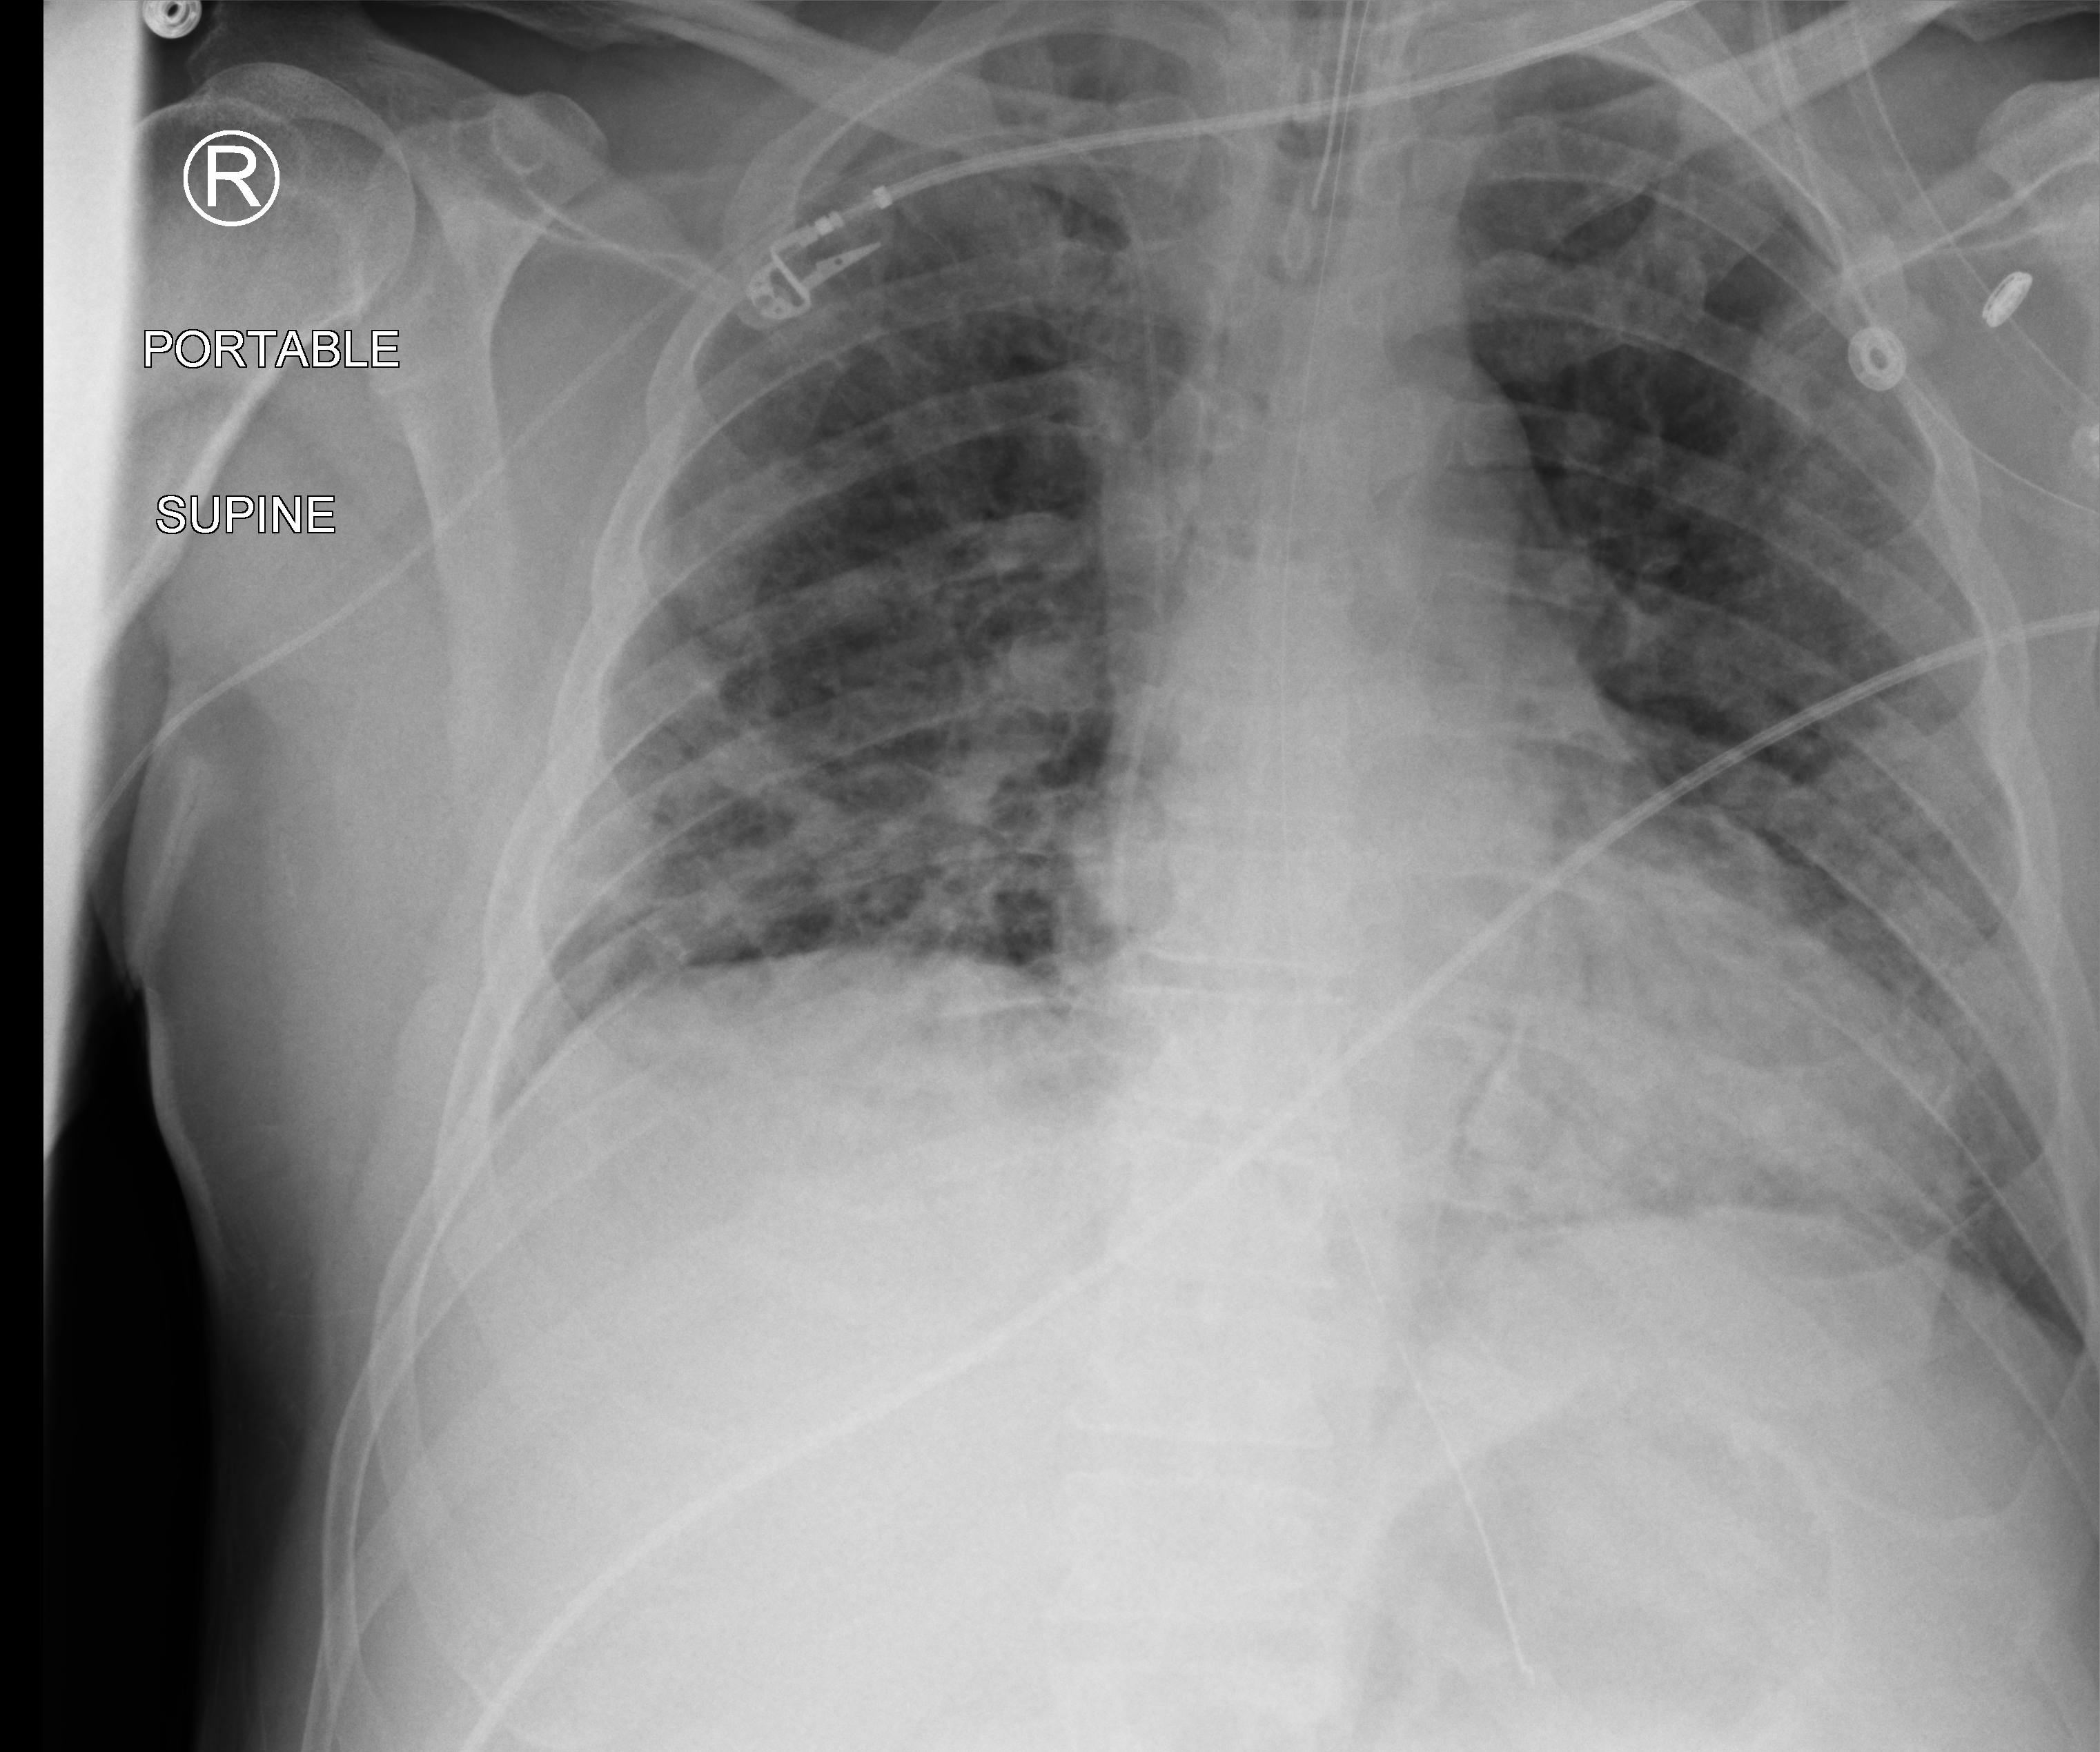
Portable chest radiograph; anteroposterior (AP) projection. Patient hospitalised with COVID-19; male, aged 18–59 years.
From the hospital-stay record, not from the radiograph (when in the stay this image was taken is not recorded): mechanically ventilated during this hospital stay: yes.